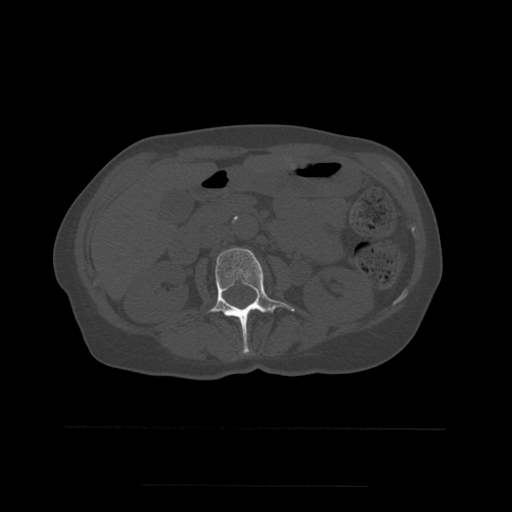
CT including the spine, one axial slice. Position 213 of 544 along the scan axis. Bone window (W 1800 / L 400 HU). 1.25 mm slice thickness. 512 × 512 image matrix, field of view 350 × 350 mm. Patient age 58 years. Case-level facts recorded for this patient, not image findings: primary cancer: lung.
Annotated regions visible in this slice (semi-automatically segmented with operator editing):
- L2 vertebra: bounding box <209,248,295,354> (left, top, right, bottom; pixels)